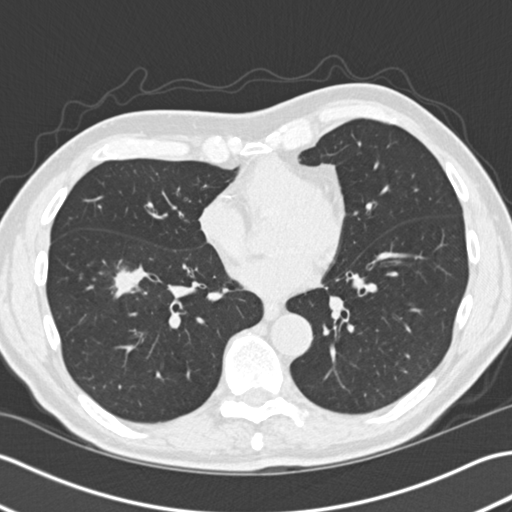
Low-dose screening chest CT, one axial slice. Position 69 of 172 along the scan axis. Reconstruction kernel B30f. Lung window (W 1500 / L -600 HU). 512 × 512 image matrix, field of view 350 × 350 mm.
Structures marked on this image (expert manual segmentation):
- lesion 1 (tumor, lower lobe of right lung): bounding box [x1, y1, x2, y2] px = [112, 265, 150, 298]